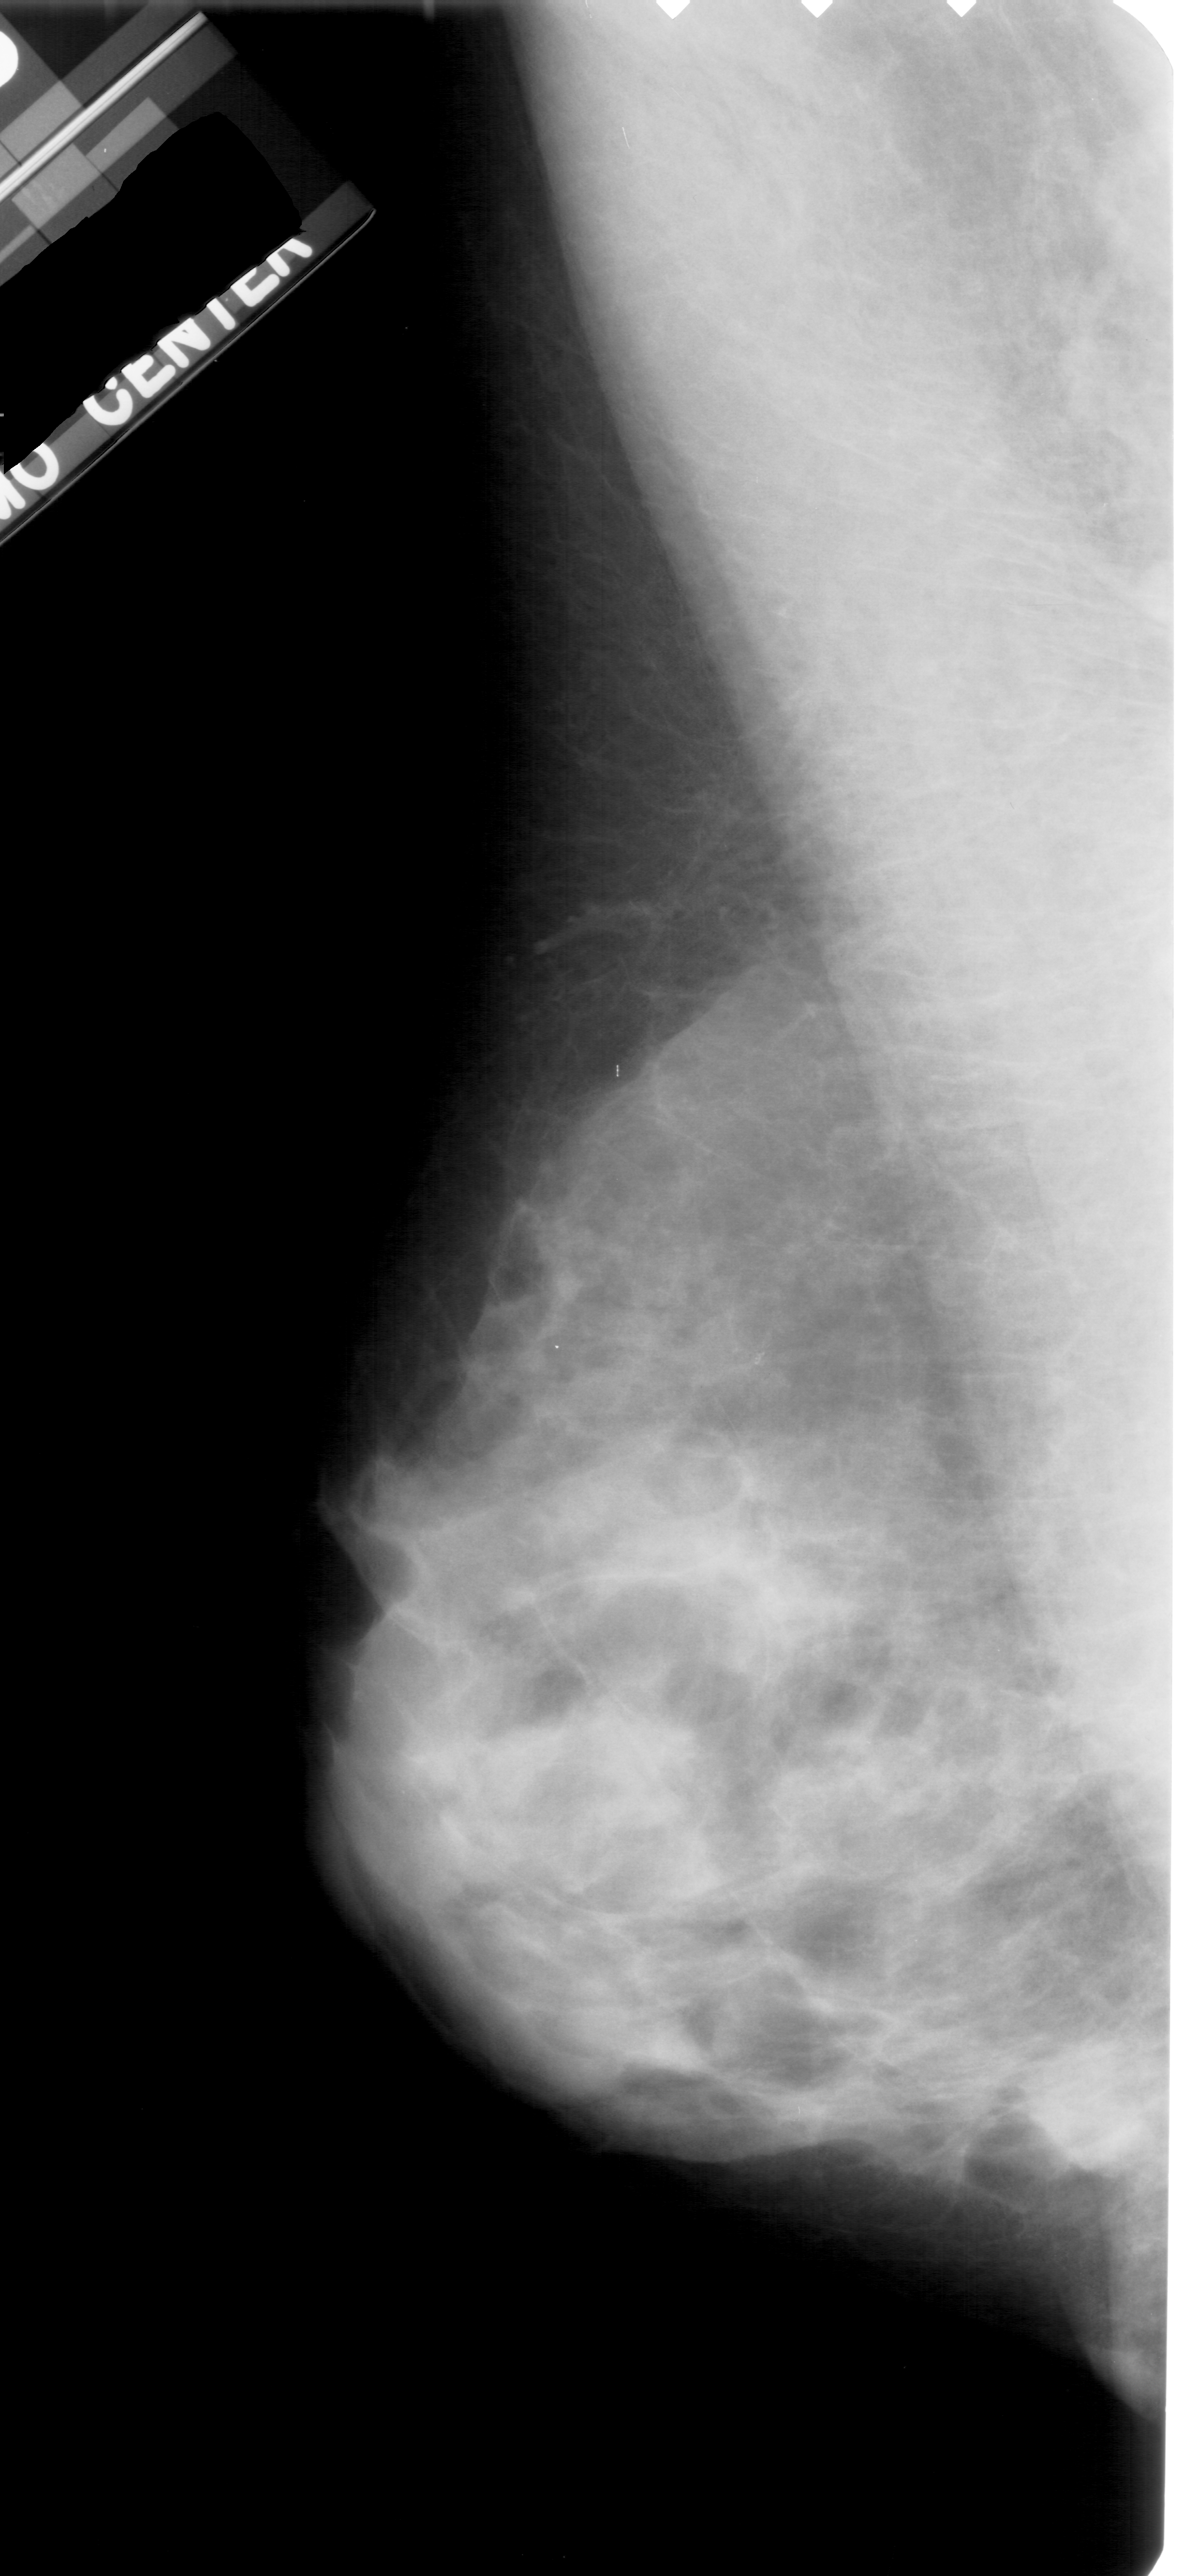
Scanned film-screen mammogram; left breast; MLO view; BI-RADS breast density category 4 (scale 1–4); 1183 × 2576 image matrix.
Expert-marked regions of interest on this film, with their recorded descriptors:
- calcifications, morphology pleomorphic, distribution clustered; BI-RADS assessment category 4; pathology result (as recorded, not read from the image): benign: bounding box (x1, y1, x2, y2) in pixels: (721, 1329, 781, 1377)